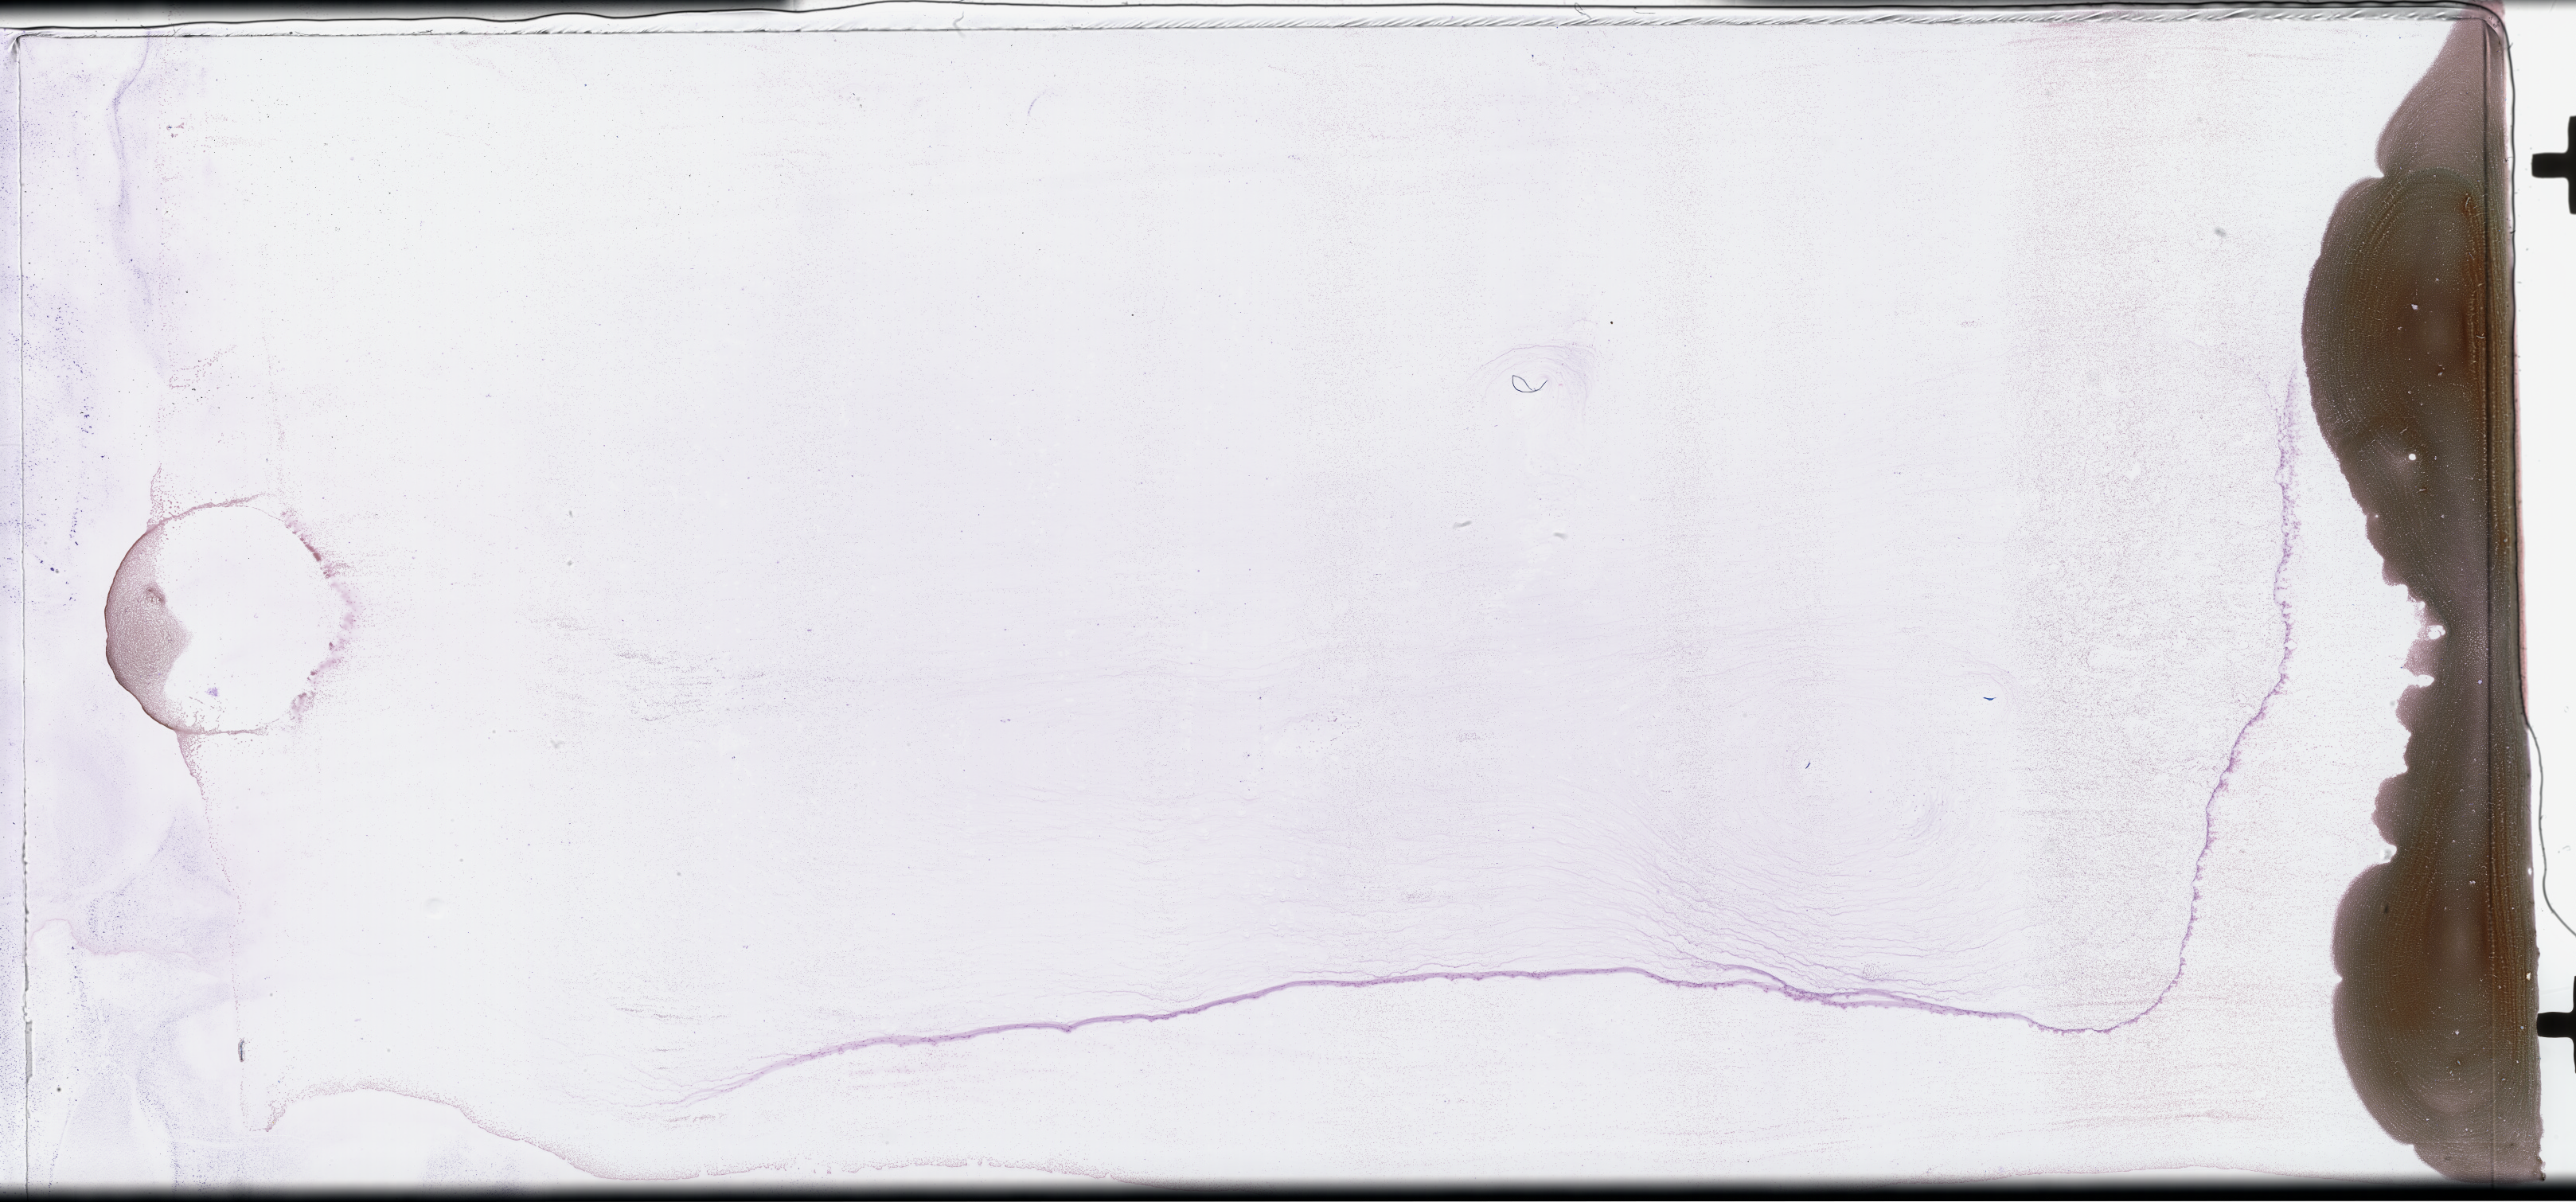
Wright–Giemsa-stained bone marrow smear, whole-slide image, a low-resolution overview of the entire scanned area, about 52.3 x 24.4 mm, EDTA-anticoagulated smear, specimen time point: collected at baseline (before treatment). Female patient.
* from a patient with: Plasma Cell Myeloma